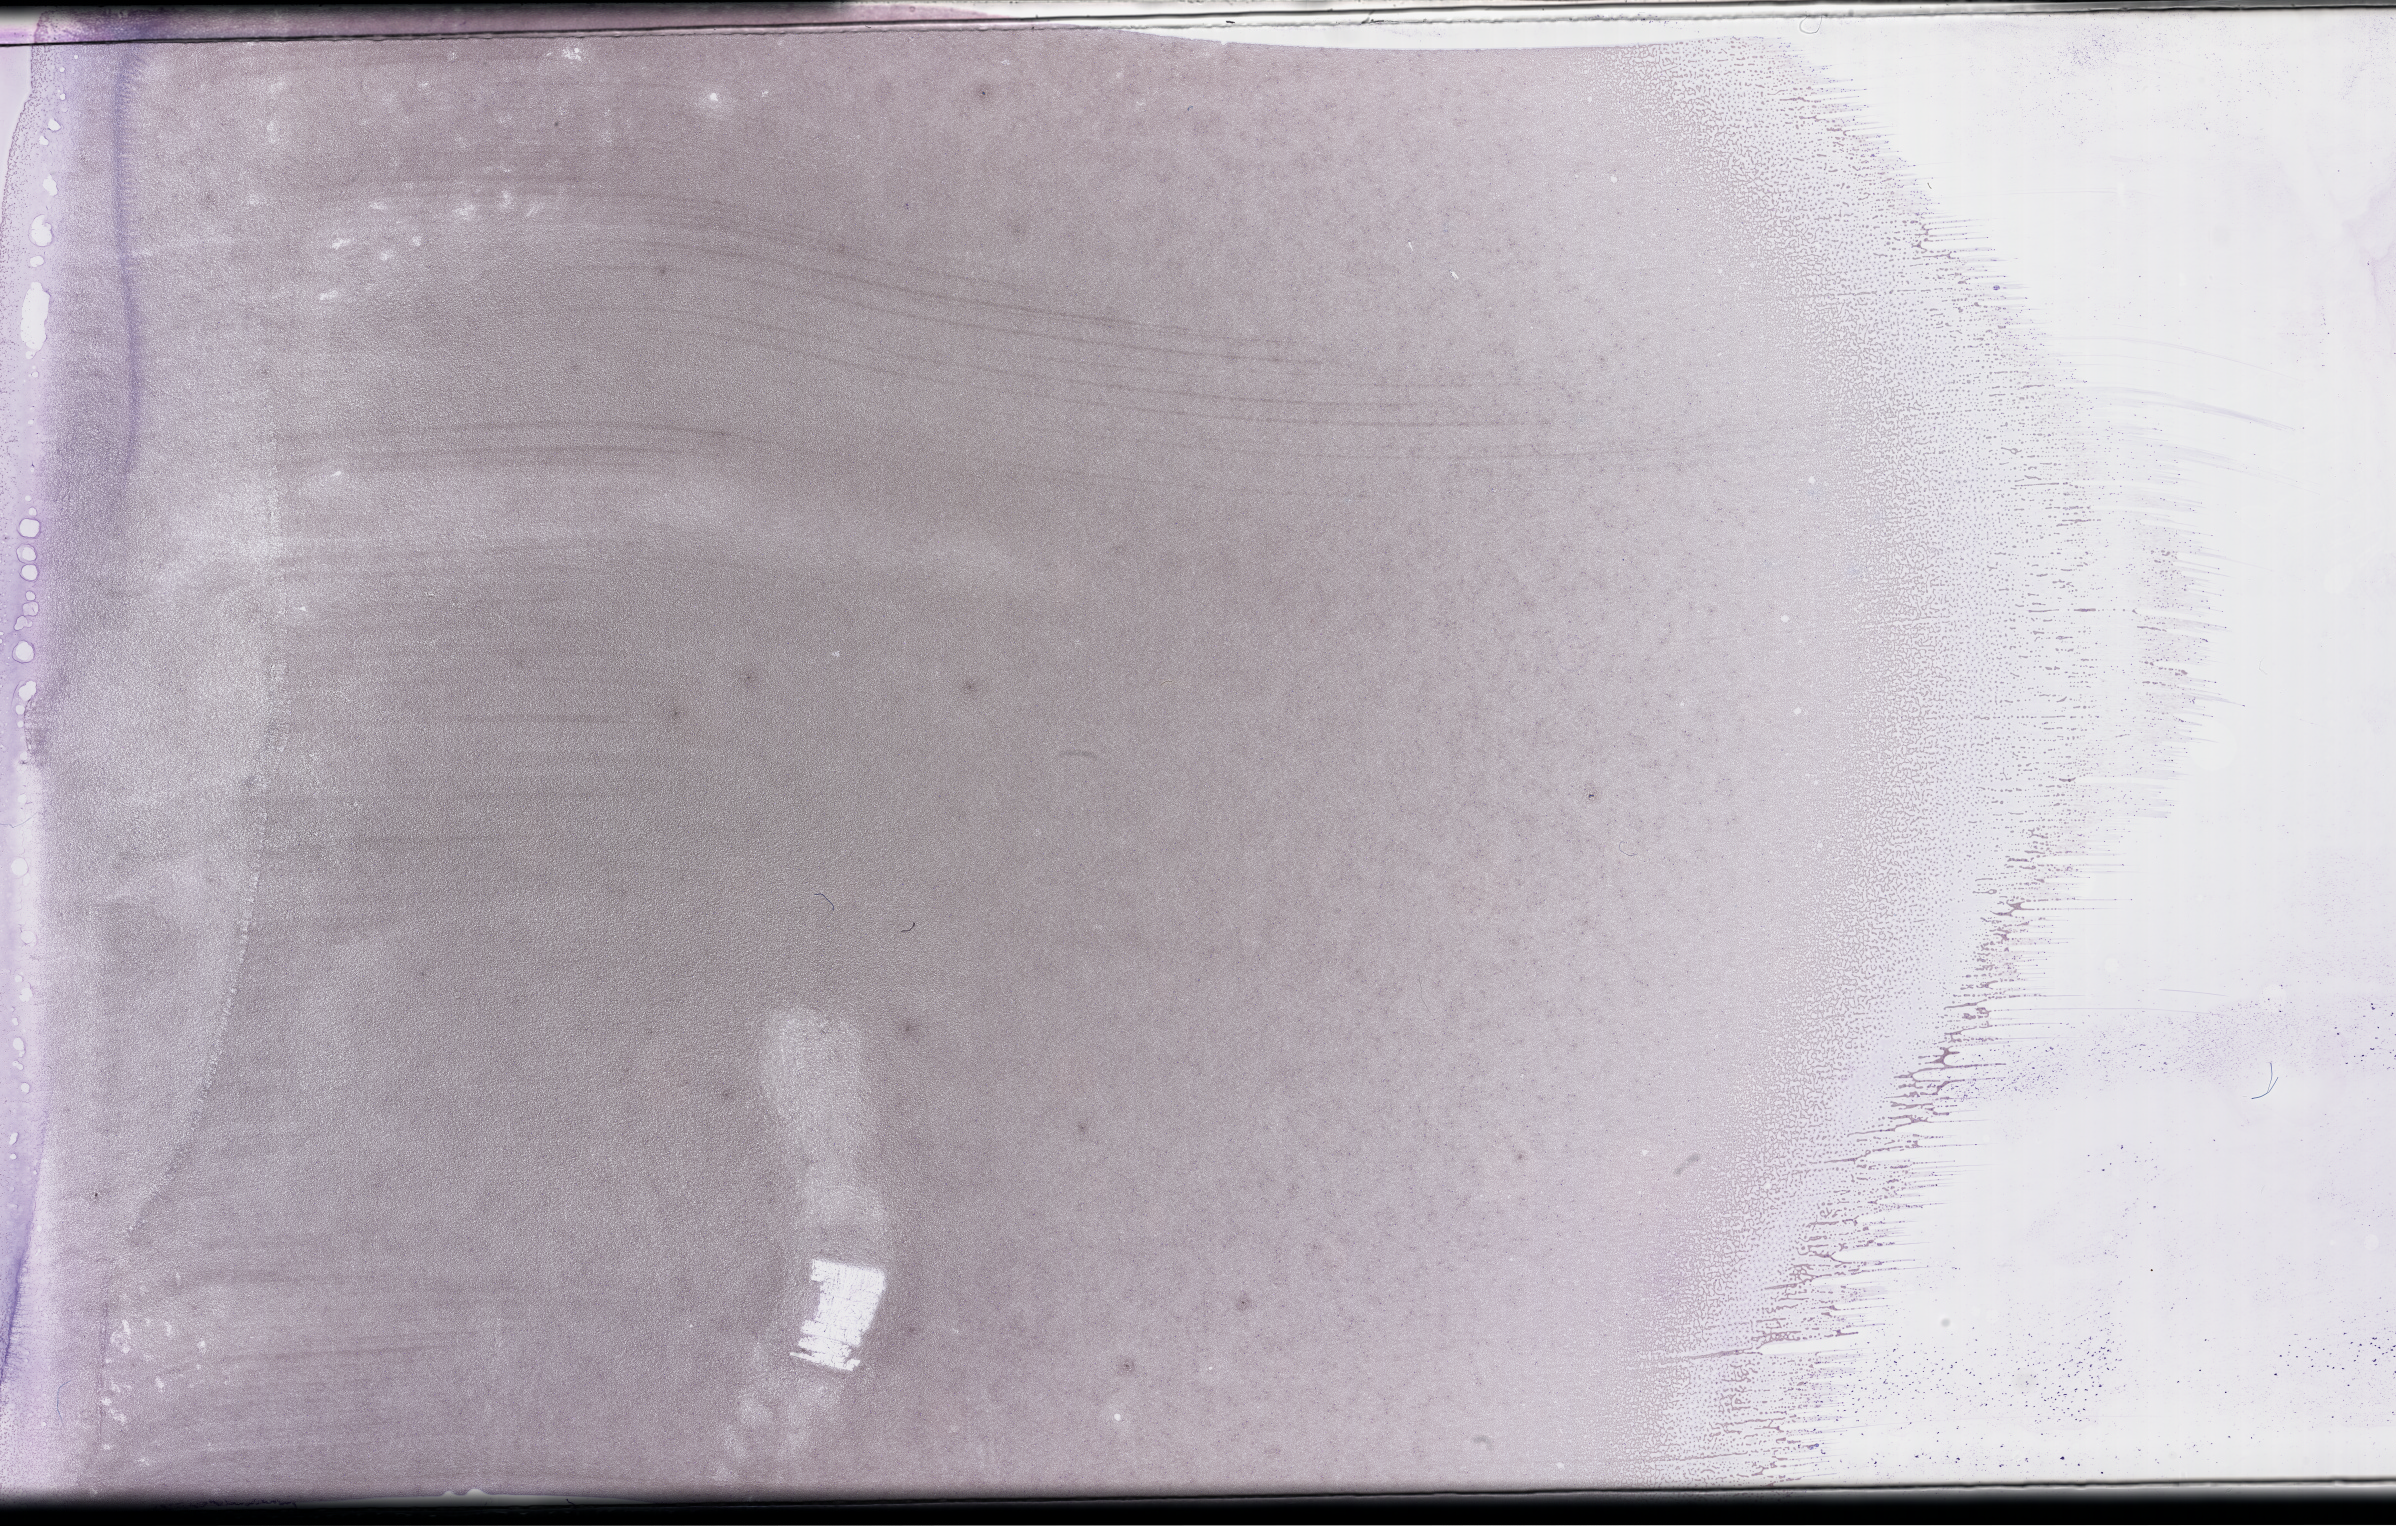
Whole-slide image of a whole blood smear, Wright–Giemsa stain — shown as a low-resolution overview of the whole scanned area (about 38.7 x 24.6 mm). Patient sex: male.
From a patient with: Plasma Cell Myeloma.